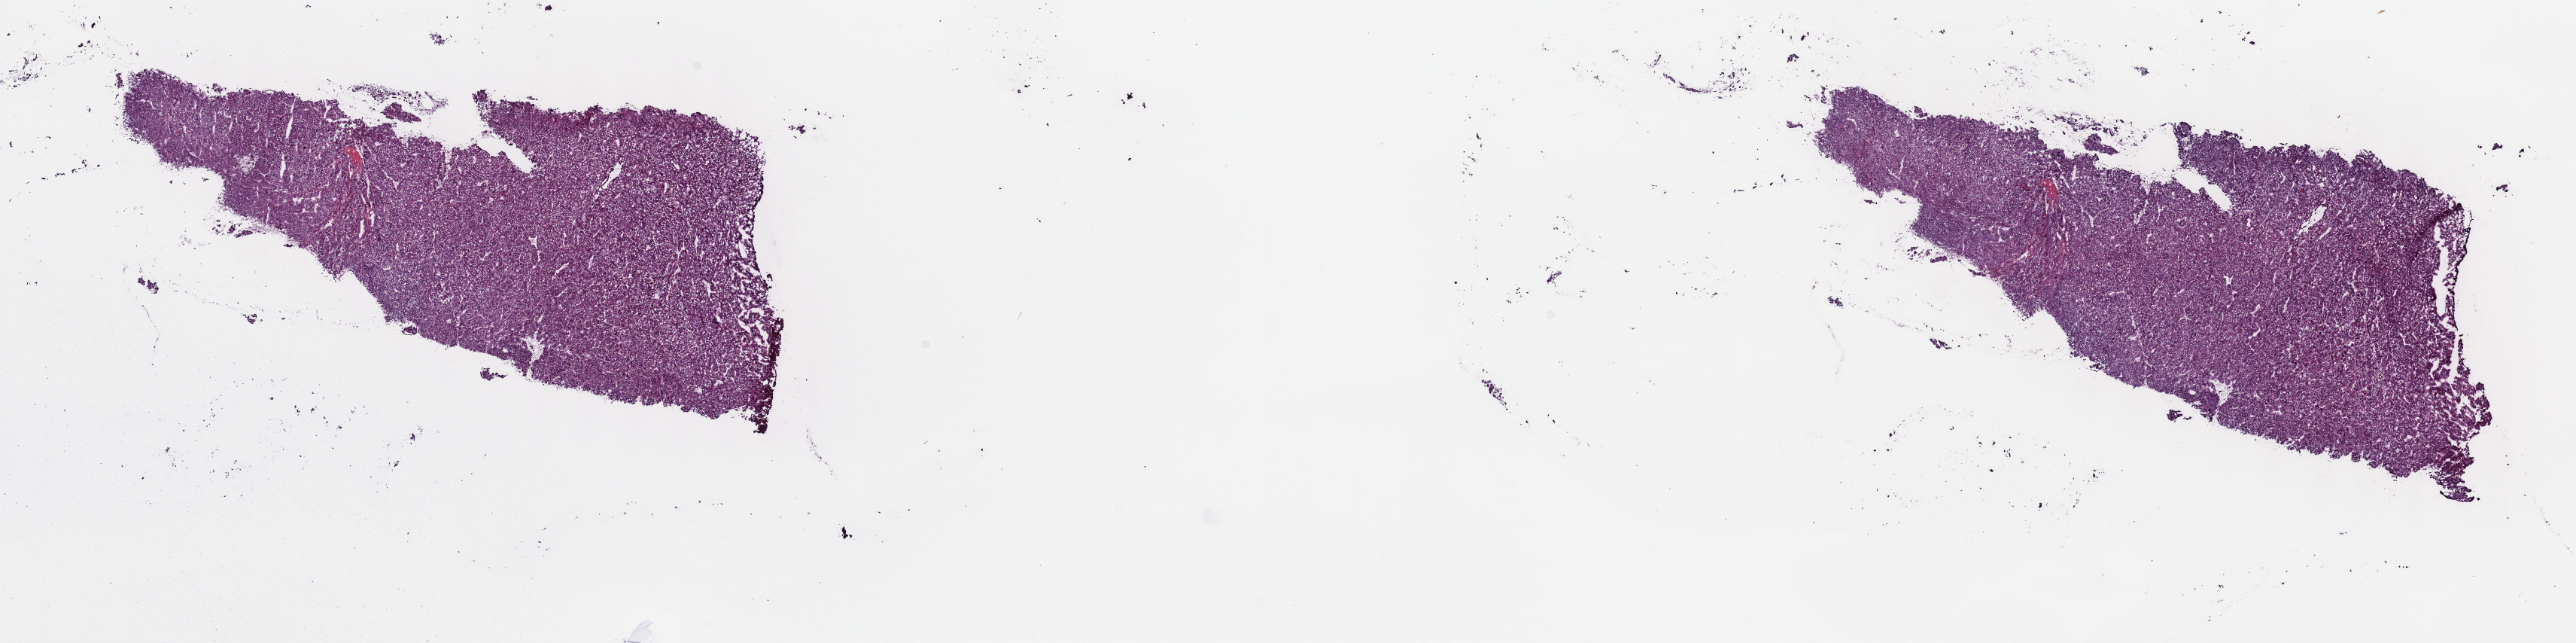
Whole-slide histology image, H&E-stained, shown as a low-resolution overview of the whole scanned area (about 27.7 x 6.9 mm); frozen section; primary tumour sample from the liver. Female patient; age at initial diagnosis 53 years.
Pathologic diagnosis: Hepatocellular carcinoma, NOS.